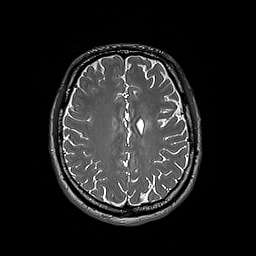
Brain MRI from a brain-tumour surgery series, one axial slice. Slice 69 of 192 in the series (ordered by position). 1 mm slice thickness. 256 × 256 image matrix. From the clinical record (not read from this slice): histopathology: Oligodendroglioma; WHO grade: 3.
Structures marked on this image (expert manual segmentation):
- tumour: bounding box <145,119,153,129> (left, top, right, bottom; pixels)